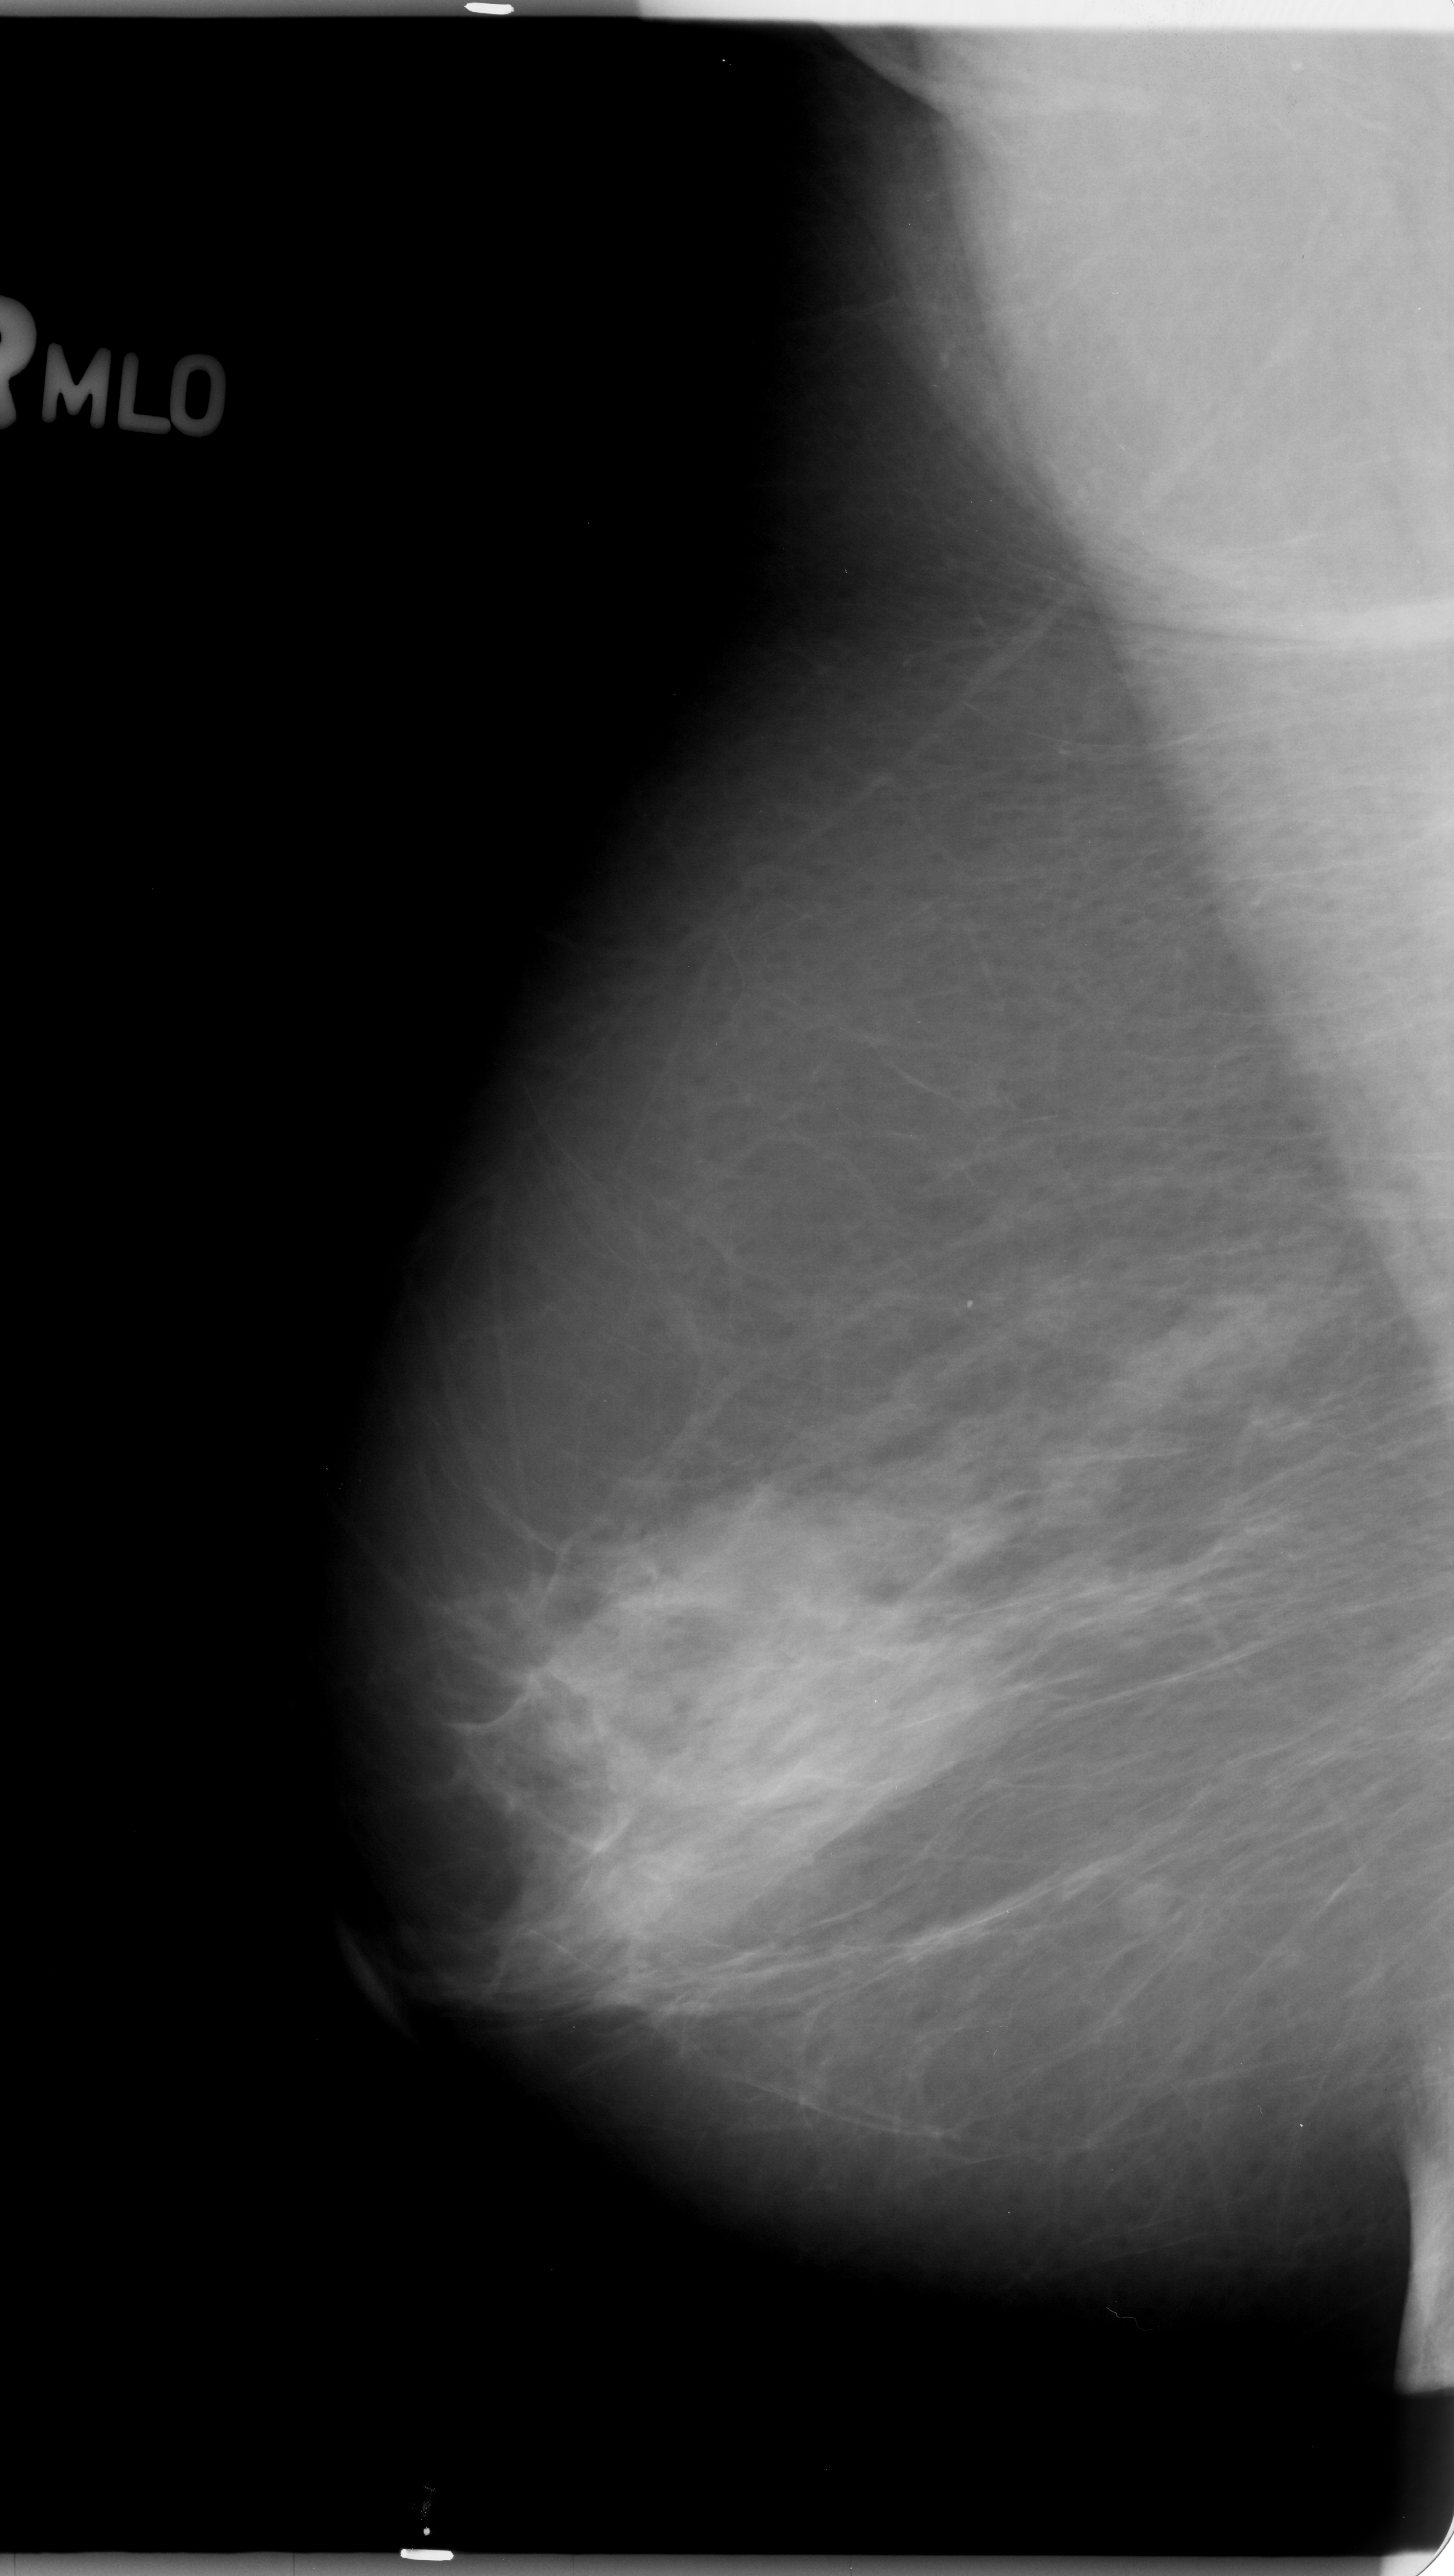
Digitized screen-film mammogram. Right breast. Mediolateral oblique (MLO) view. 1454 × 2576 image matrix.
Expert-marked regions of interest on this image (one box per marked abnormality):
- mass, shape irregular, margins ill defined; BI-RADS assessment category 4; pathology (as recorded): benign: bounding box (x1, y1, x2, y2) in pixels: (1096, 1858, 1191, 1957)